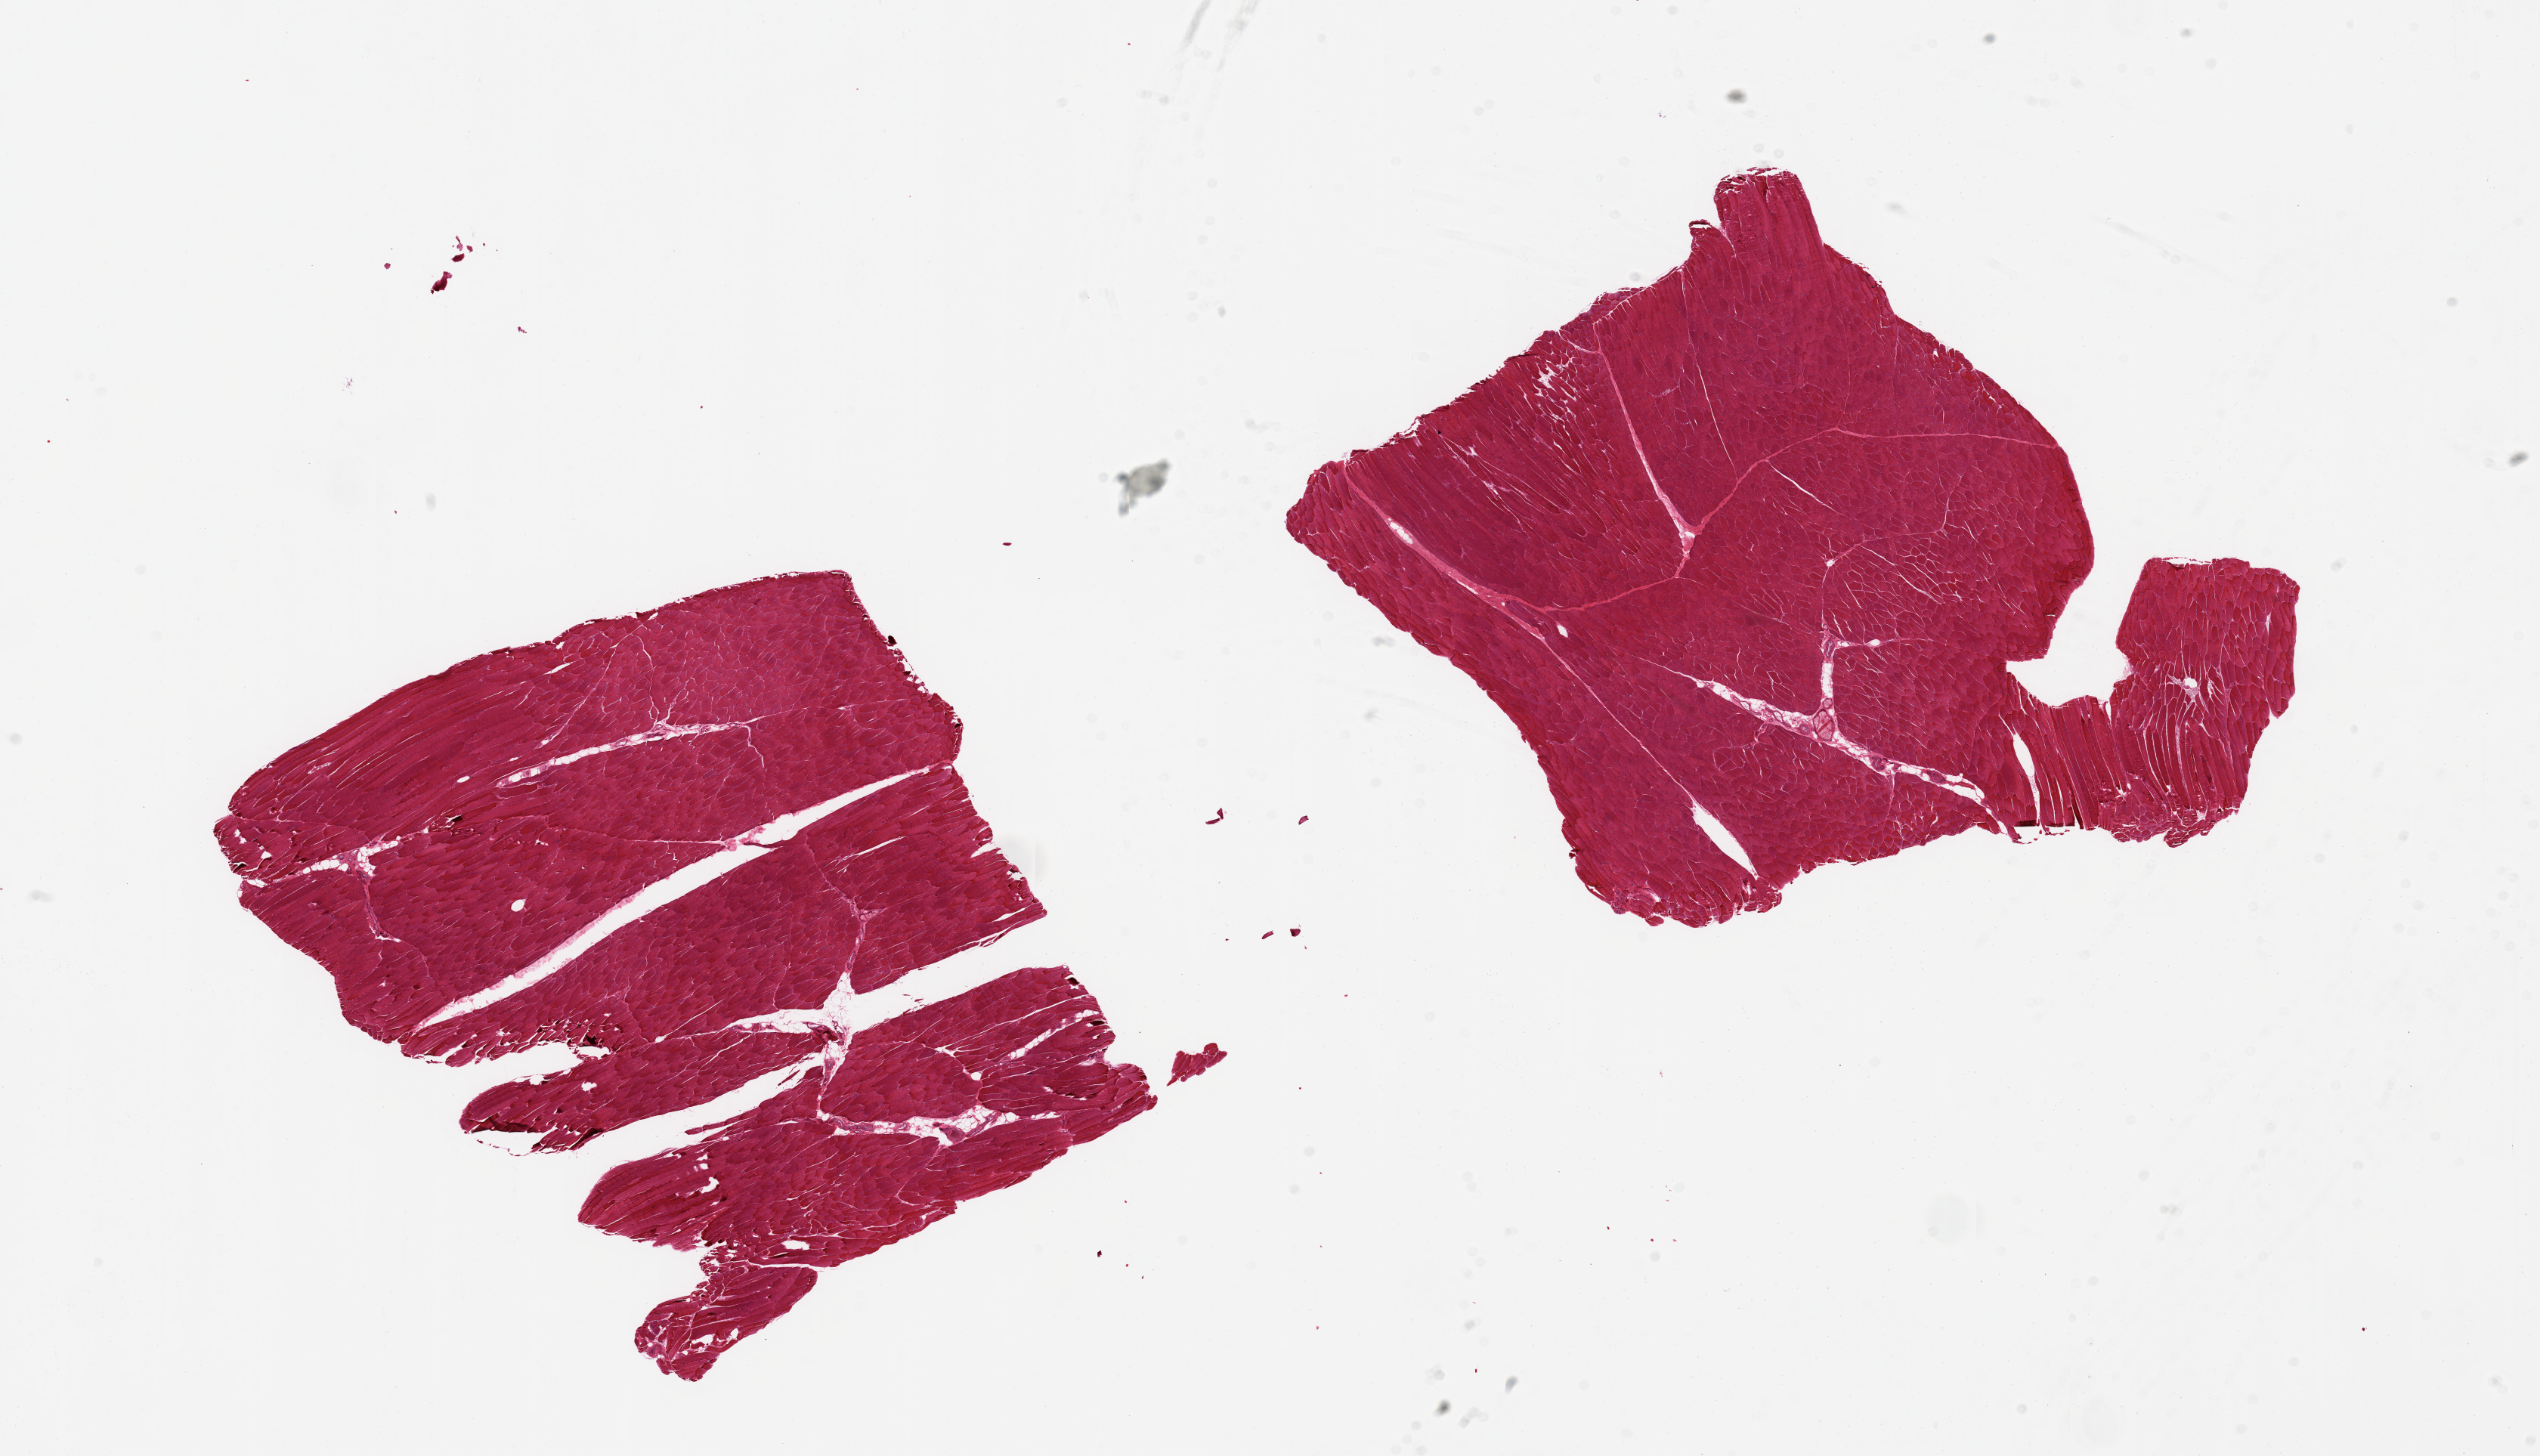
Whole-slide image, haematoxylin and eosin stain, brightfield — whole scanned area (about 26.6 x 15.2 mm) shown as a low-resolution overview, PAXgene-fixed, paraffin-embedded tissue, target tissue: skeletal muscle, tissue donor sample. Donor: male.
Reviewer comment on this tissue sample: 2 pieces.